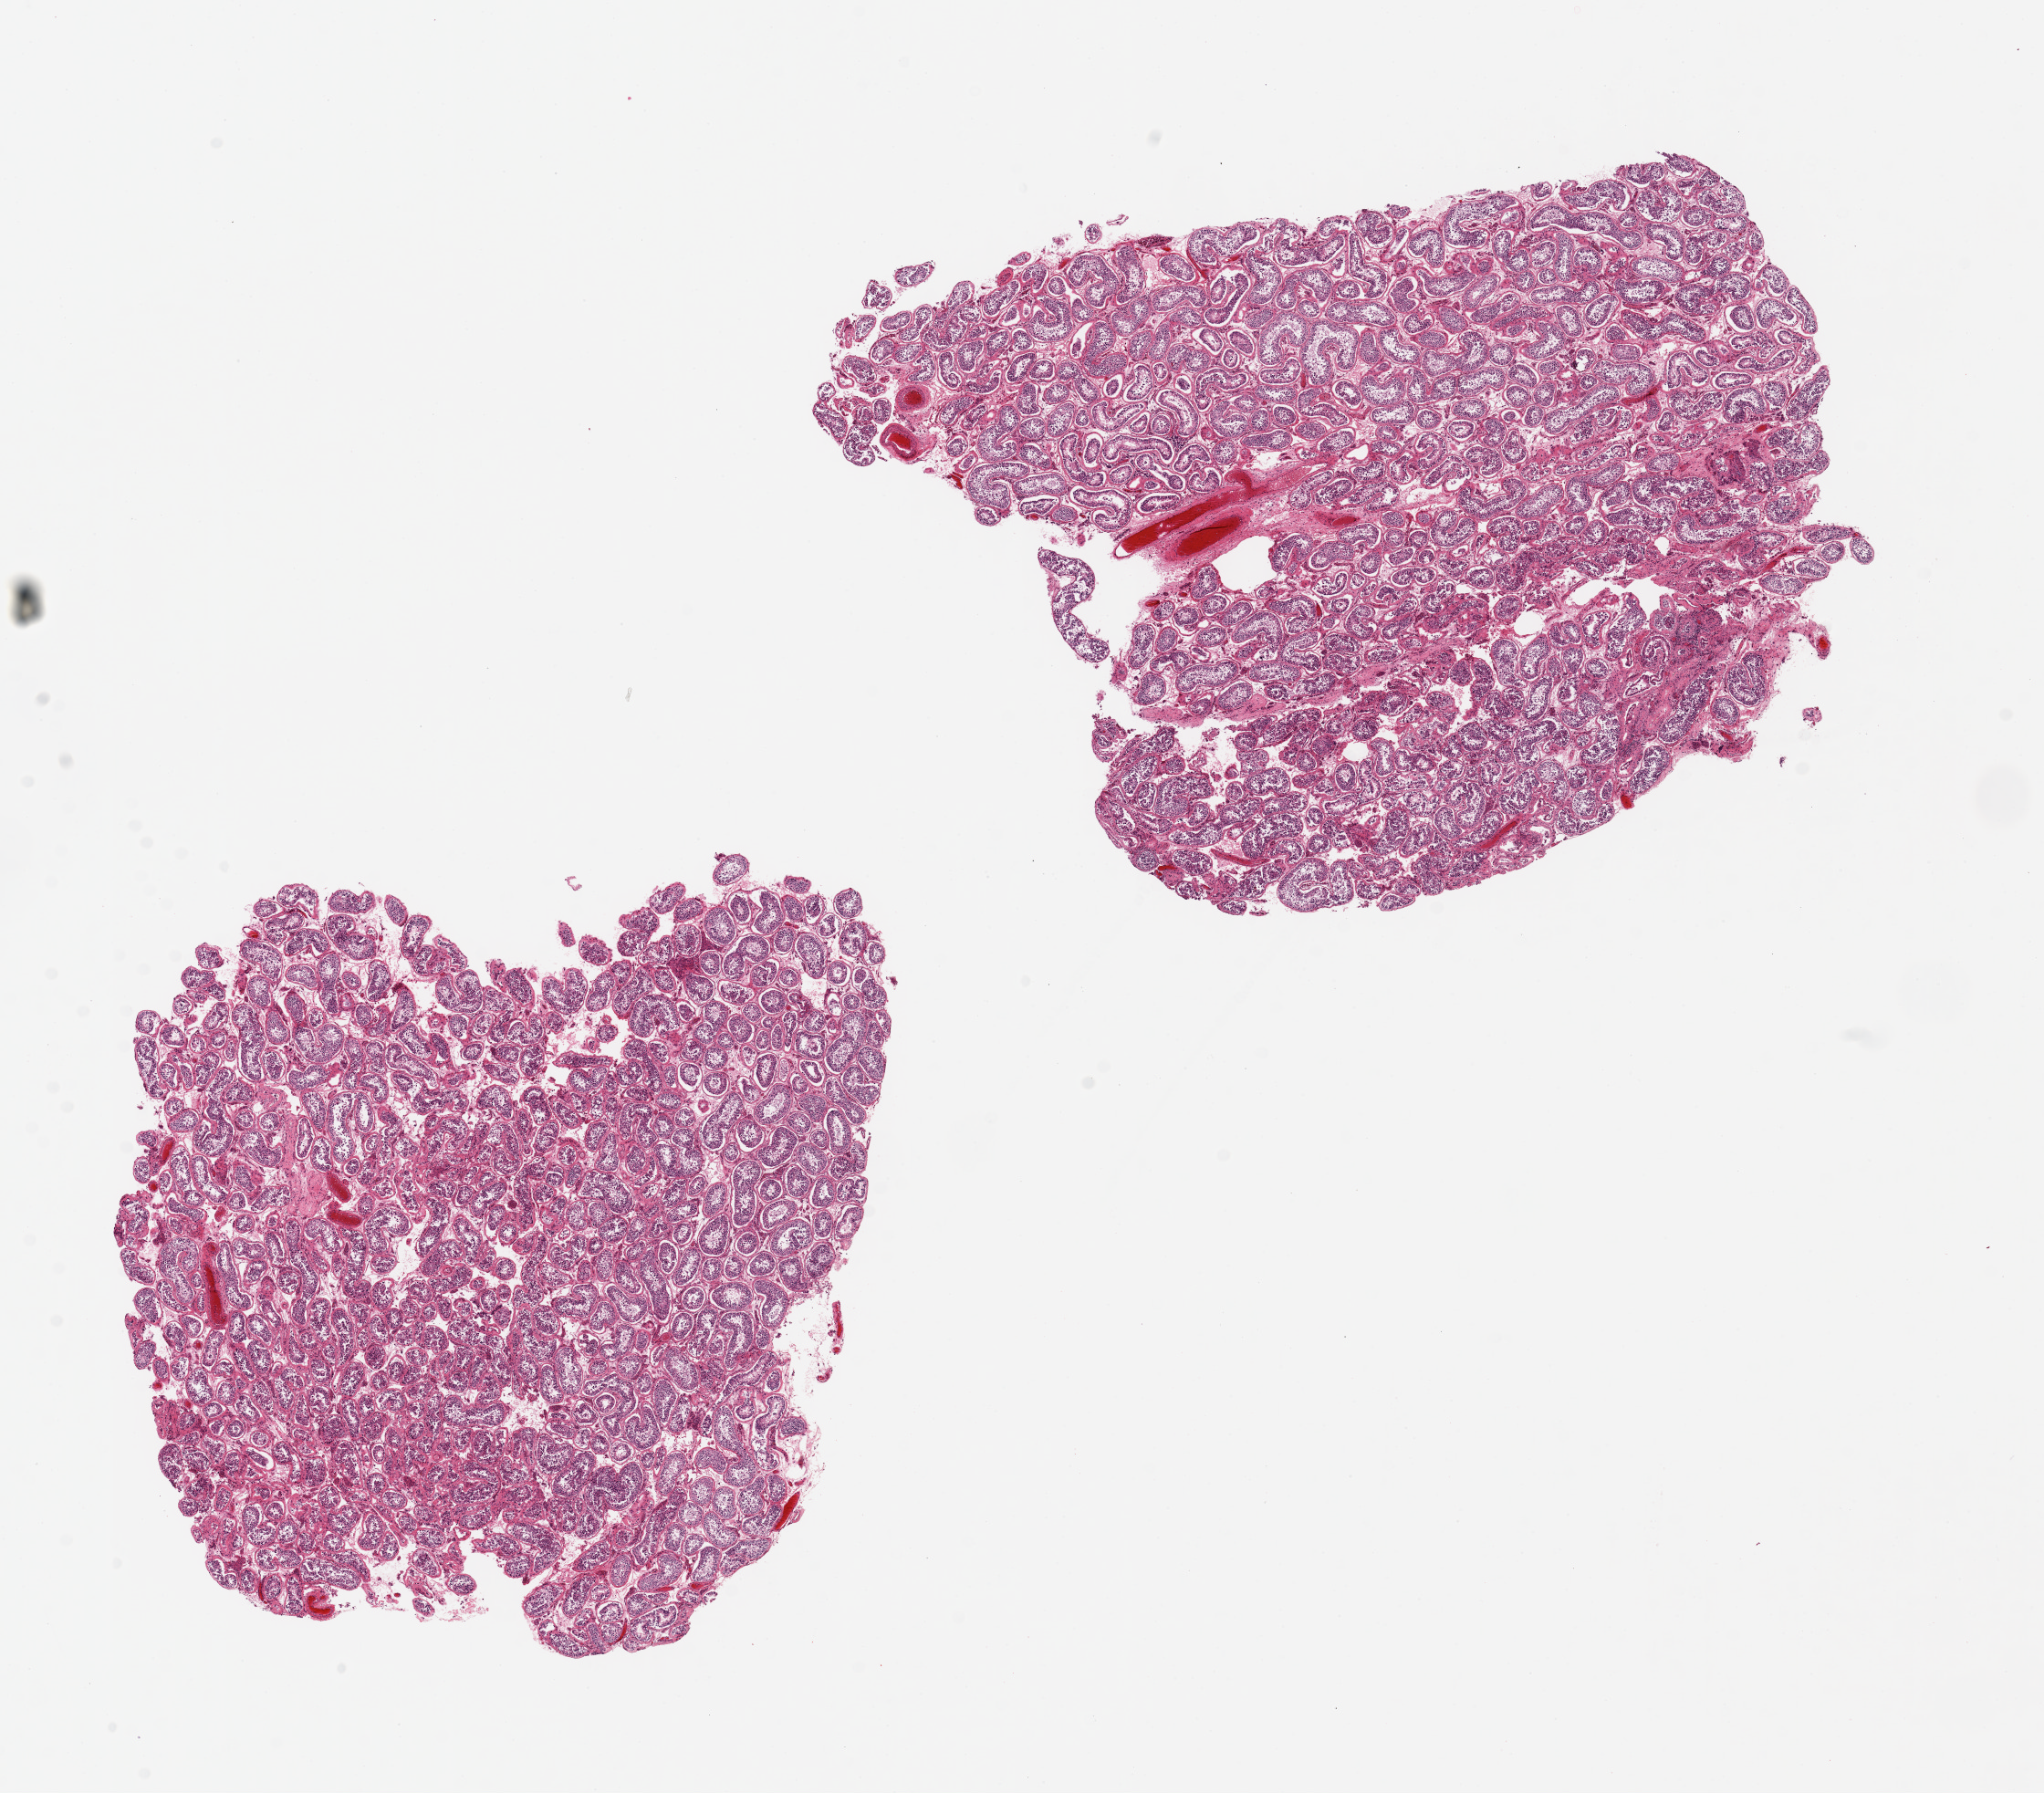
Whole-slide image, hematoxylin and eosin (H&E) stain, whole scanned area (about 17.7 x 15.5 mm) shown as a low-resolution overview; PAXgene-fixed paraffin-embedded (PFPE) section; section of testis (target tissue); donor tissue sample. Male donor.
Reviewer comment on this tissue sample: 2 pieces ~8x6mm. Spermatogenesis is presnet but reduced.